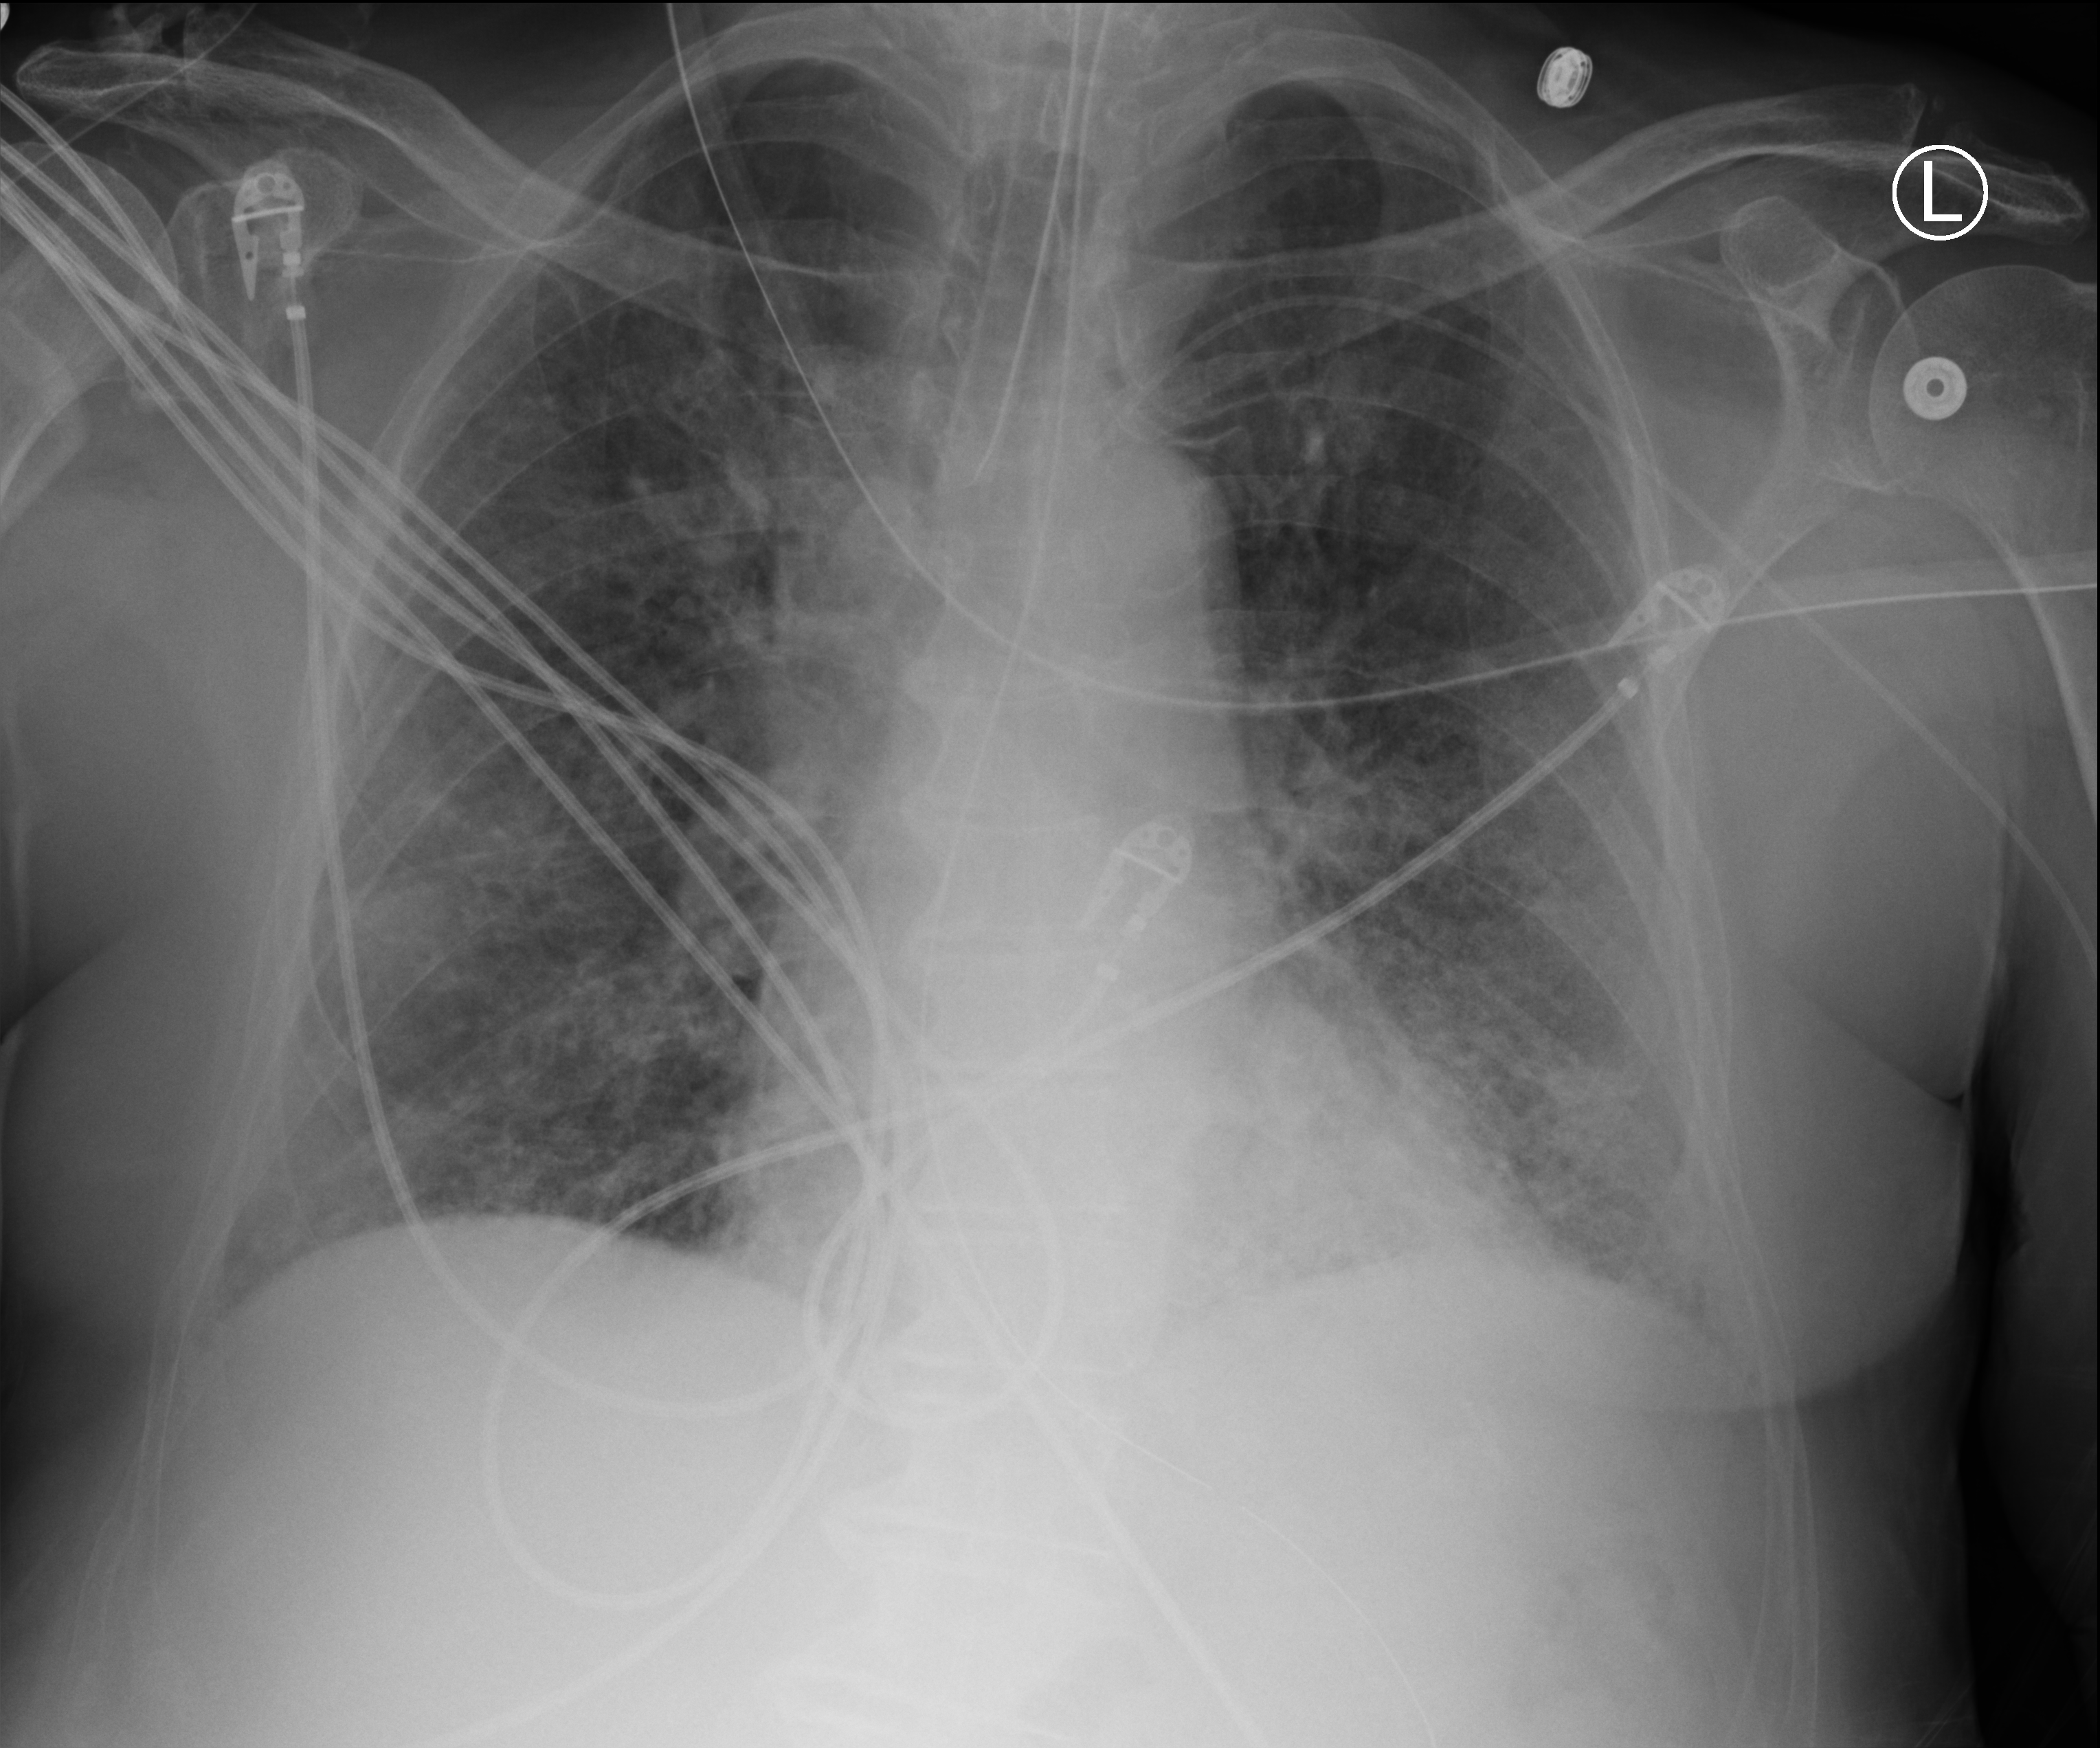
Chest X-ray (portable); anteroposterior (AP) projection. Patient hospitalised with COVID-19; male, aged 75–90 years.
From the hospital-stay record, not from the radiograph (when in the stay this image was taken is not recorded):
- mechanically ventilated during this hospital stay: yes